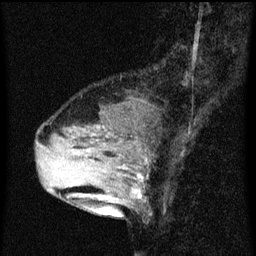
Breast MRI (dynamic contrast-enhanced), one sagittal slice; slice 21 of 60 in the series (ordered by position); dynamic contrast-enhanced series, image 2 of 3 at this slice position (ordered by acquisition); 1.5 T; TE 4.2 ms, TR 8 ms; 256 × 256 image matrix, field of view 180 × 180 mm. Female patient, age 33 years.
Annotated regions visible in this slice (semi-automatically segmented with operator editing):
- analysis volume of interest (the breast-tissue region the enhancement analysis was run in; not a lesion): bounding box (x1, y1, x2, y2) in pixels: (61, 126, 149, 213)
- tumour enhancement mask (voxels above the 70 % enhancement threshold inside the analysis volume of interest): (93, 160, 143, 197)